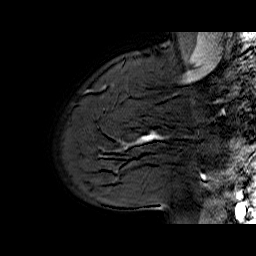
Breast MRI (dynamic contrast-enhanced), one sagittal slice; slice 51 of 70 in the series (ordered by position); dynamic contrast-enhanced series, time point 2 of 6 at this slice position (early post-contrast); 1.5 T; TE 6.5 ms, TR 33 ms; 4 mm slice thickness; 256 × 256 image matrix, field of view 200 × 200 mm. Female patient. From the clinical record (not read from this slice): setting: breast cancer imaged before/during neoadjuvant chemotherapy; receptor status: HER2-positive.
Outlined on this slice (semi-automatically segmented with operator editing):
- analysis volume of interest (the breast-tissue region the enhancement analysis was run in; not a lesion): bounding box <113,112,174,170> (left, top, right, bottom; pixels)
- tumour enhancement mask (voxels above the 100 % enhancement threshold inside the analysis volume of interest): <138,132,157,141>